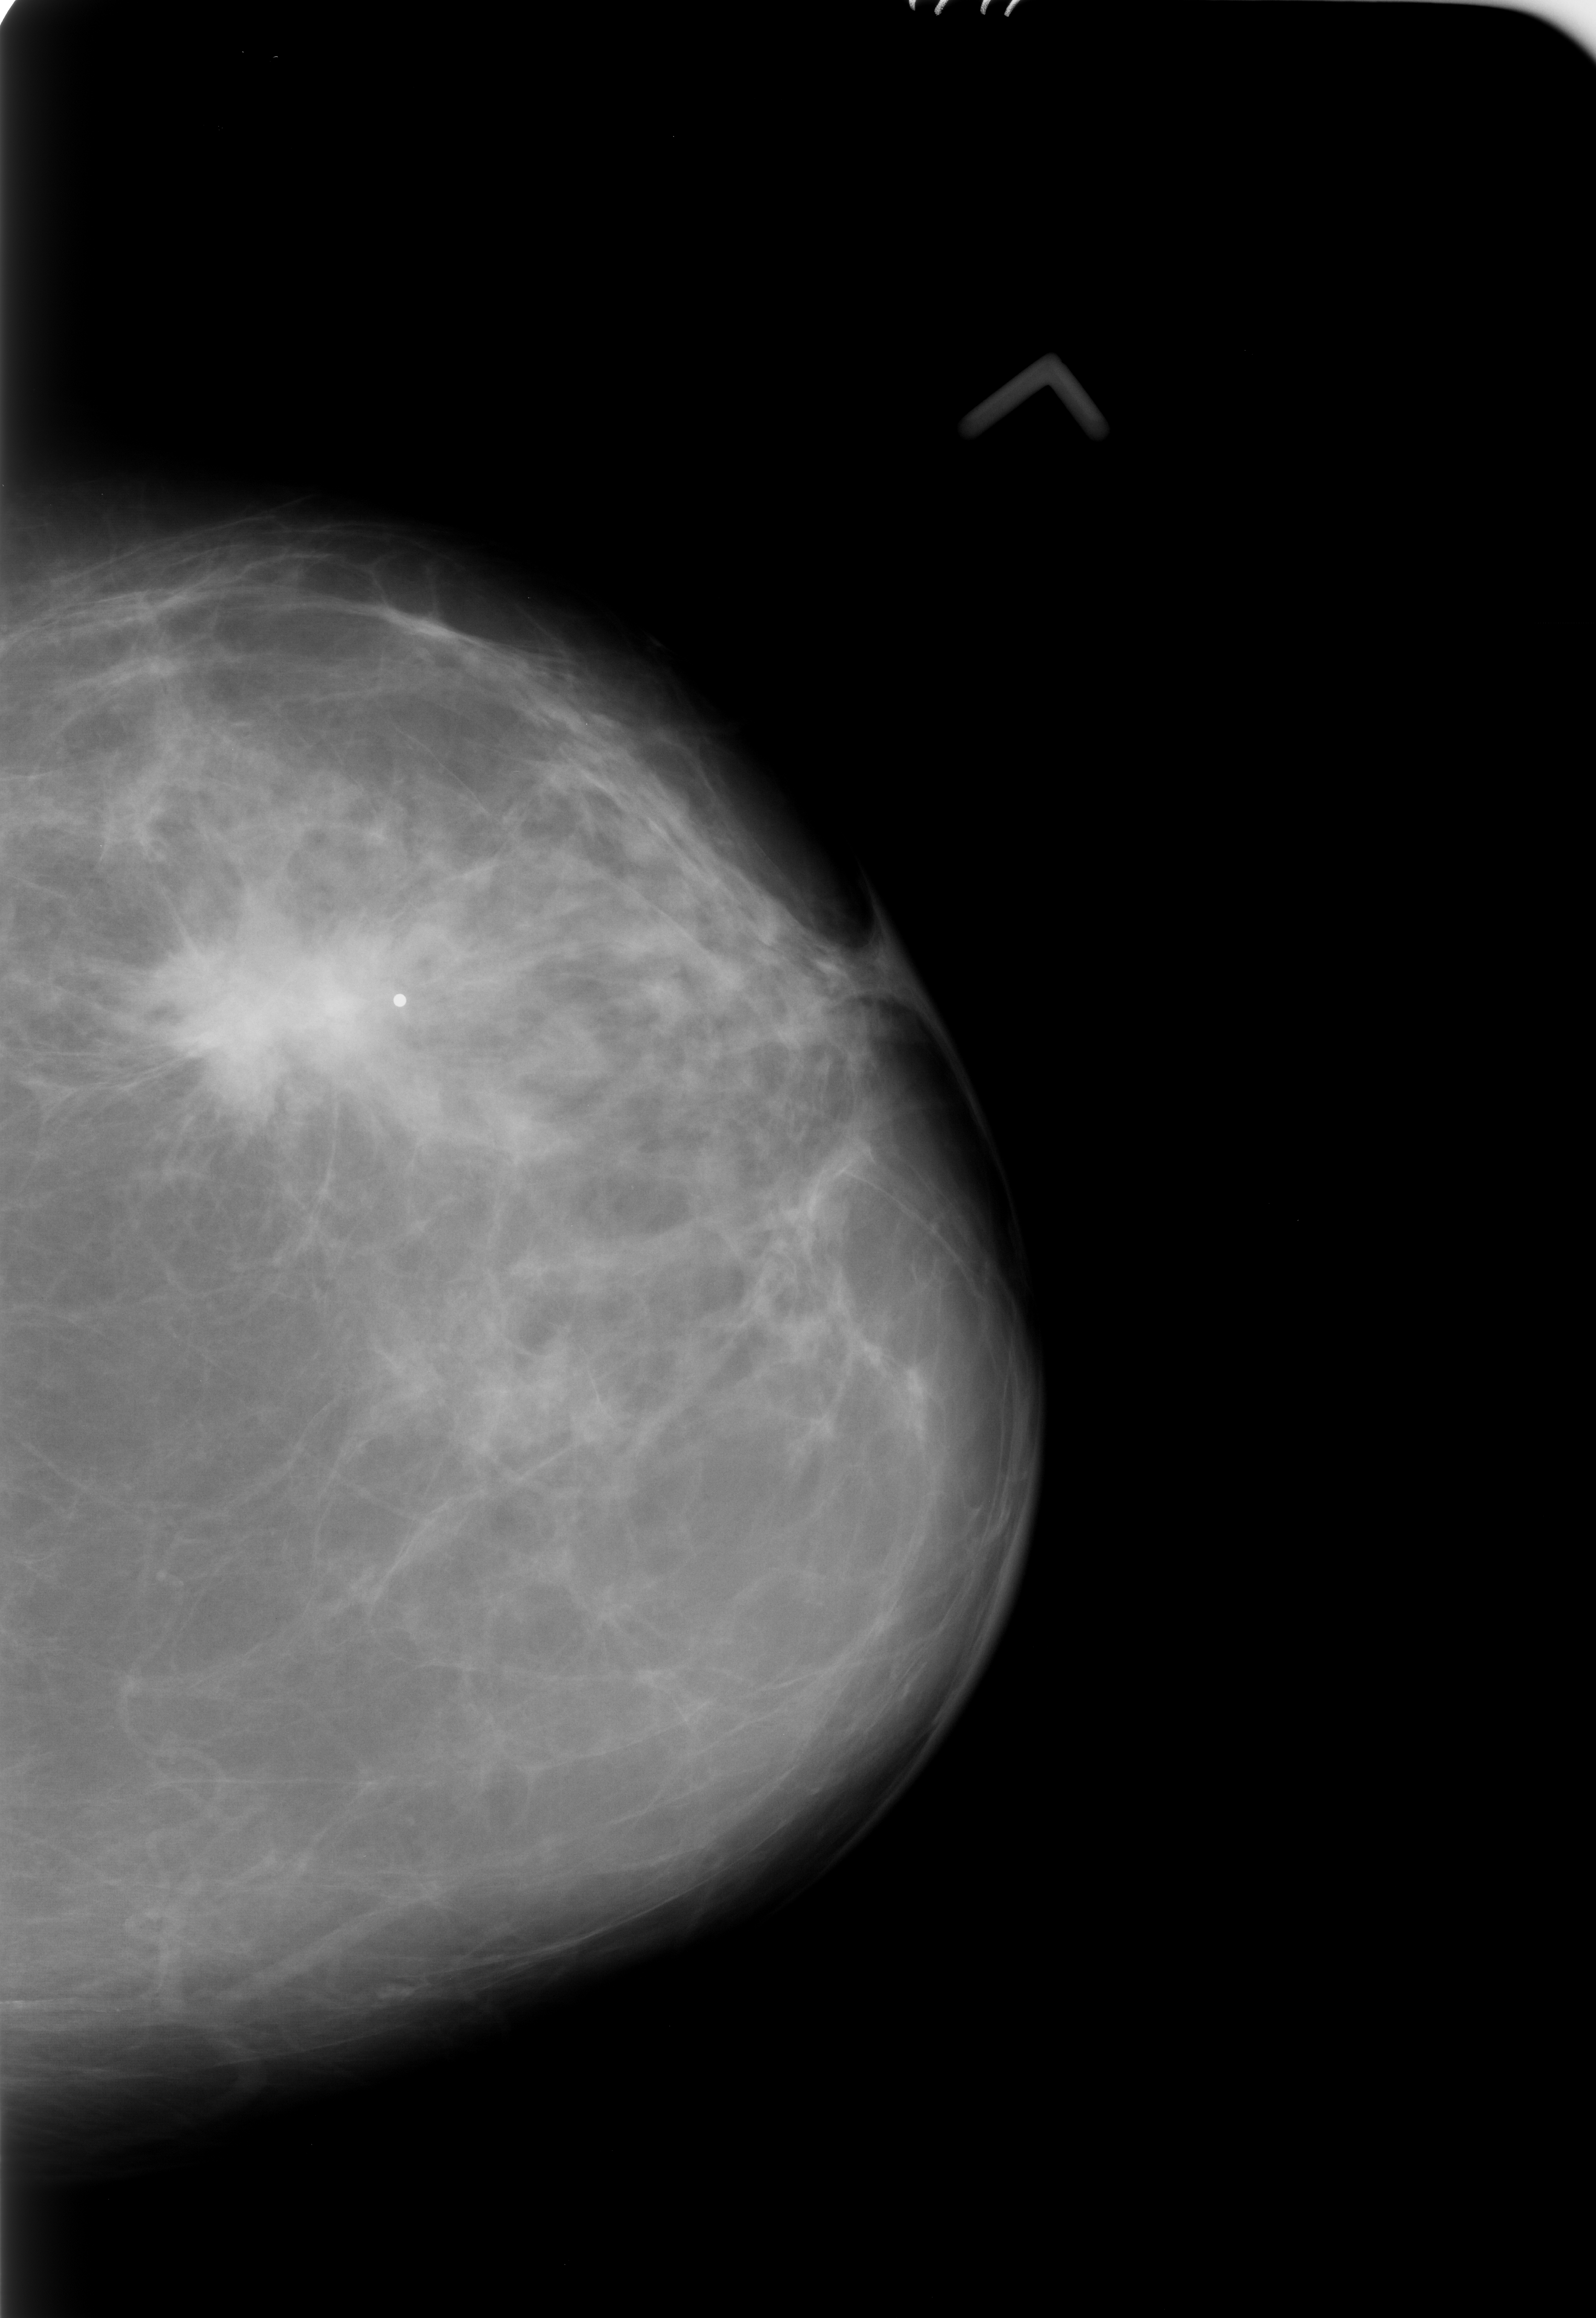
Mammogram (digitized film). Left breast. Craniocaudal (CC) view. Breast composition: scattered fibroglandular densities (BI-RADS density category 2 of 4). 1596 × 2318 image matrix.
Expert-marked regions of interest on this image (one box per marked abnormality):
- mass, shape irregular / architectural distortion, margins spiculated; BI-RADS assessment category 5; pathology result (as recorded, not read from the image): malignant: box from (x=166, y=924) to (x=374, y=1085) px